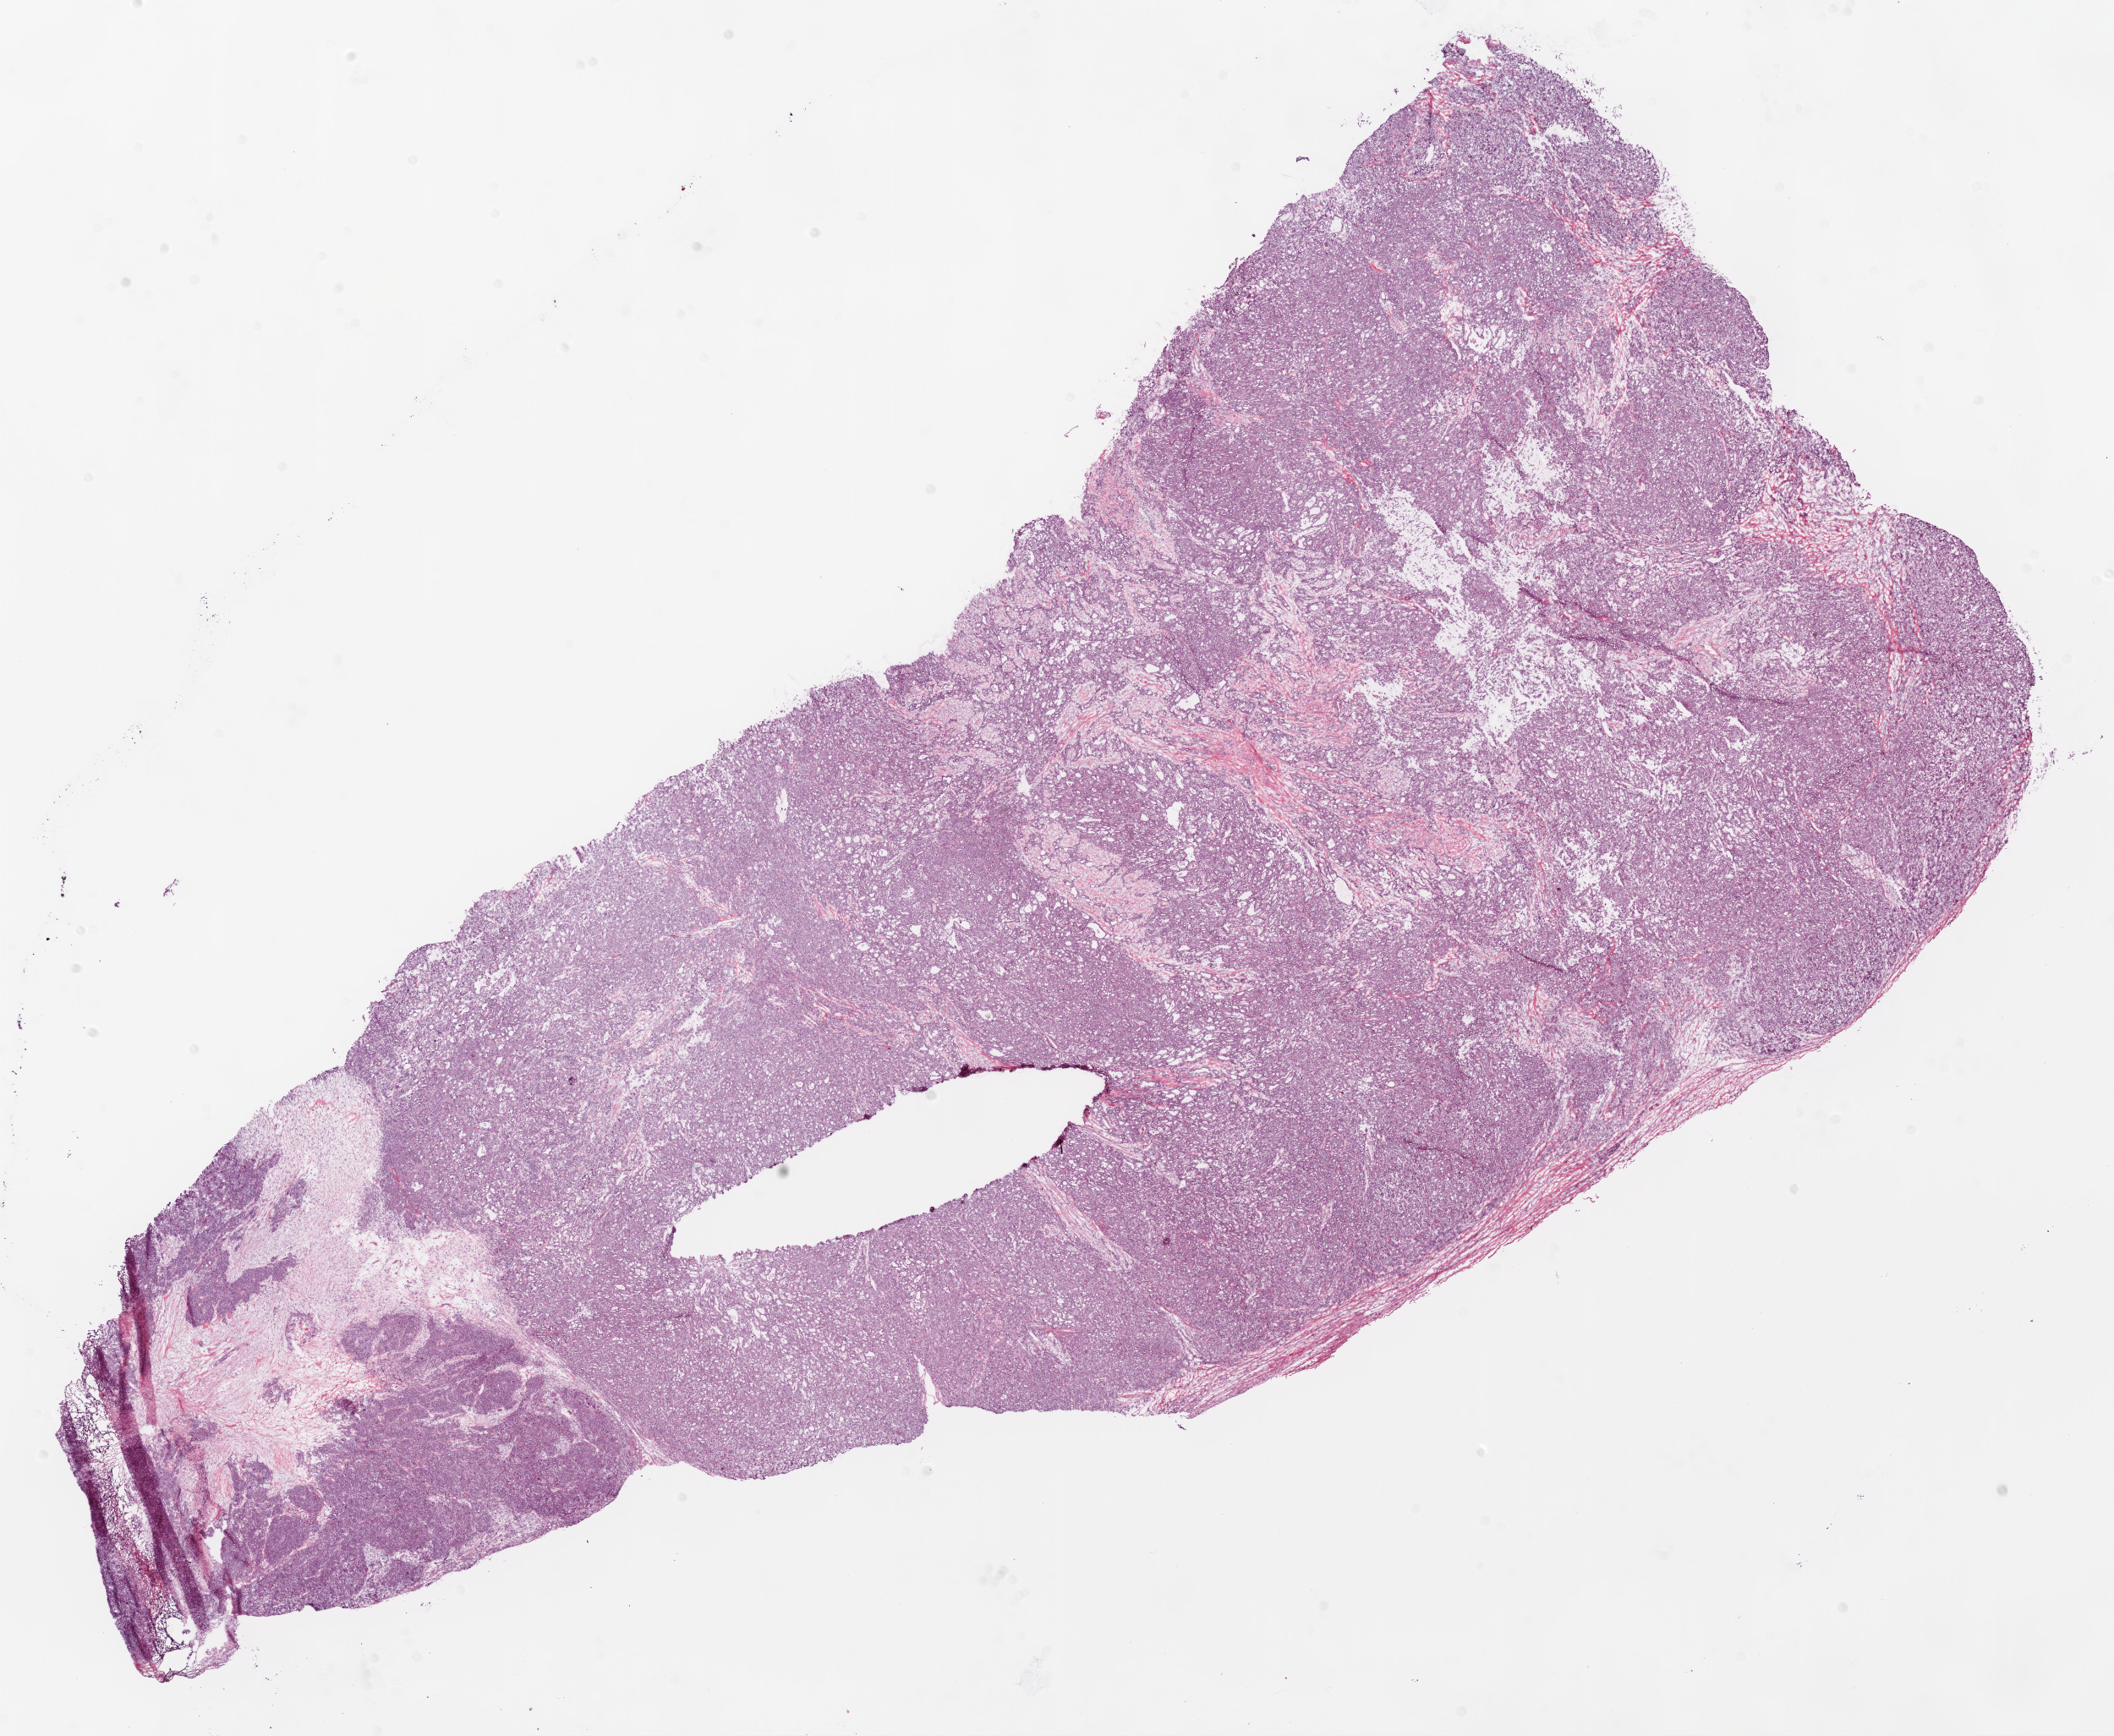
Whole-slide histology image, Hematoxylin and eosin (H&E) stained — shown as a low-resolution overview of the whole scanned area (about 20.1 x 16.5 mm, from a 20x scan), frozen section from the bottom of the tissue portion, primary tumour sample from the ovary. Female, age 55 years at initial diagnosis. Histologic grade: G3 (poorly differentiated). Pathologist review of this section (percent, as recorded): tumour cells 94%, tumour nuclei 95%, normal cells 0%, stromal cells 5%, necrosis 1%.
Pathologic diagnosis: Serous cystadenocarcinoma, NOS. FIGO stage: IIA.